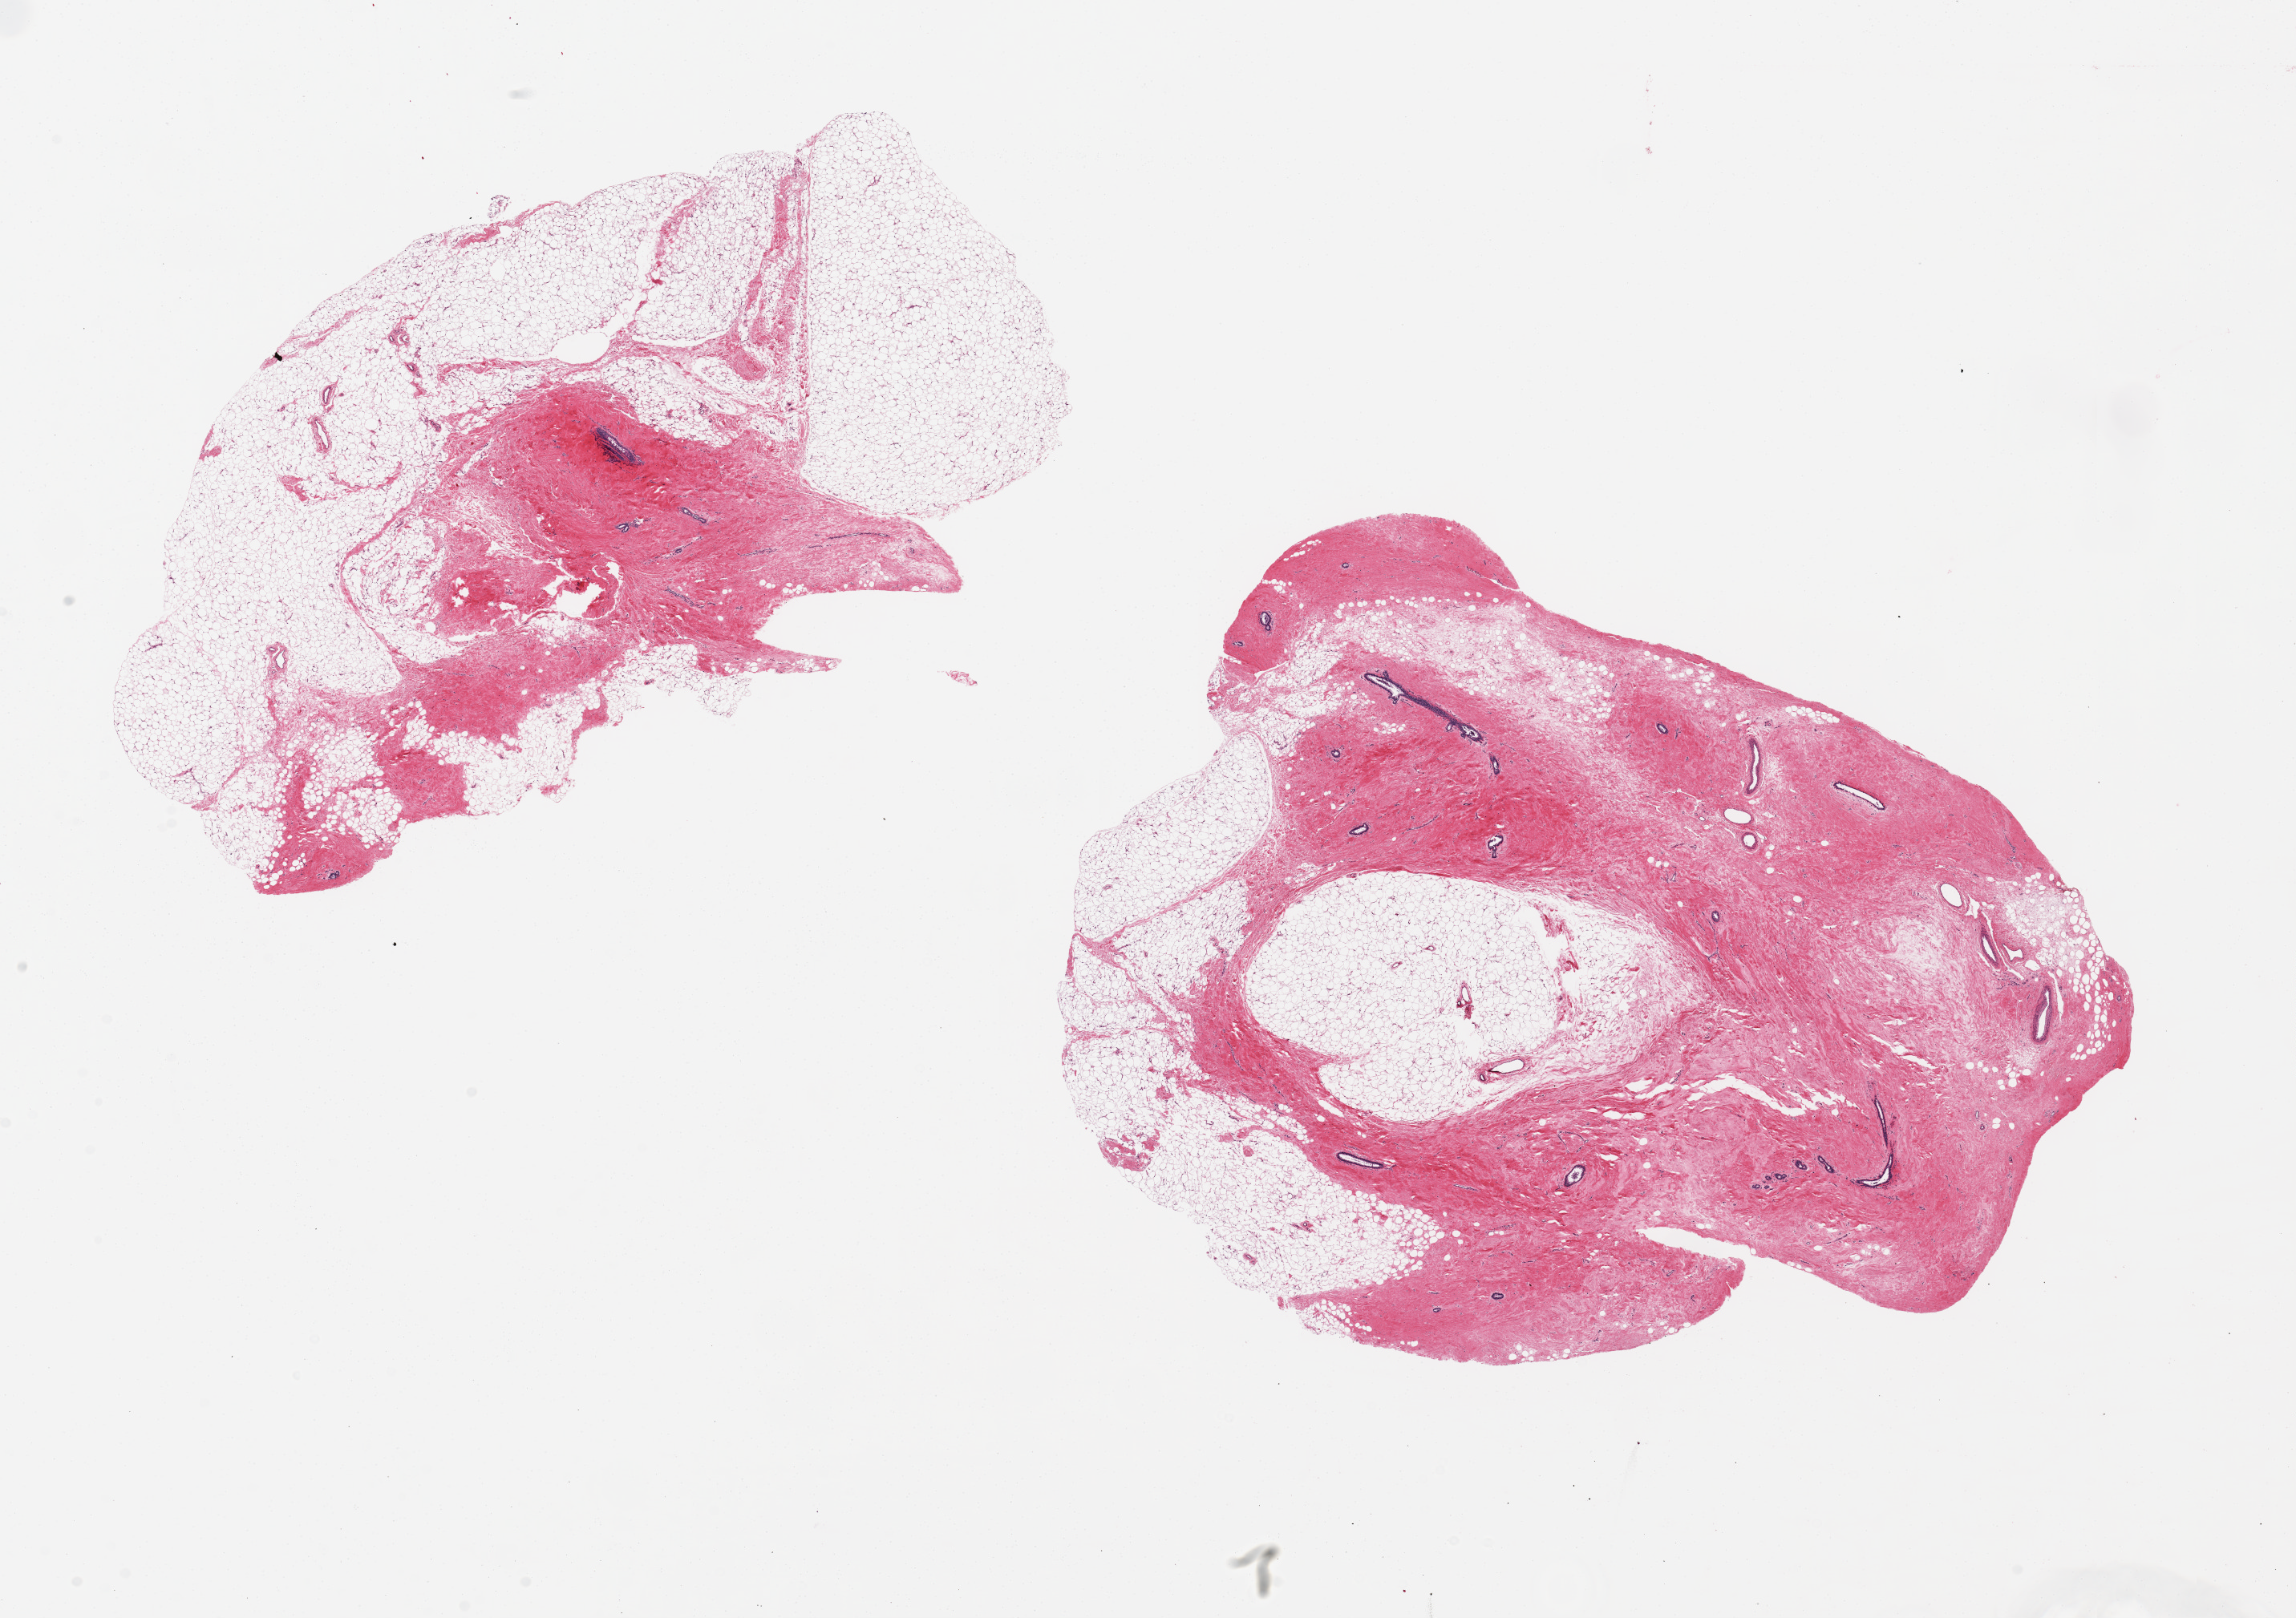
H&E whole-slide image, brightfield, low-resolution overview of the scanned area, about 22.6 x 16.0 mm (slide scanned at 20x); PAXgene-fixed paraffin-embedded (PFPE) section; section of breast (target tissue); donor tissue sample.
Pathologist's review note for this sample: 2 ~9.5x6.5mm aliquots. Ductal elements visible in both.